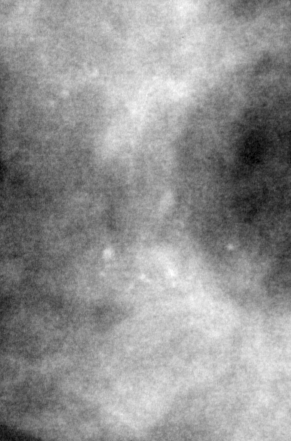
Cropped region of a digitized screen-film mammogram centred on a radiologist-marked abnormality, left breast, MLO view, BI-RADS breast density category 3 (scale 1–4).
- Calcifications, morphology pleomorphic, distribution clustered; BI-RADS assessment category 4; pathology result (as recorded, not read from the image): malignant.